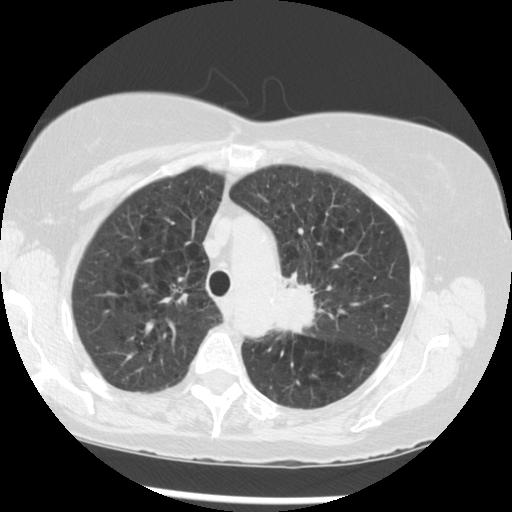
Axial slice from a low-dose chest CT screening exam, third annual screen, lung window (W 1500 / L -600 HU), 2.5 mm slice thickness, standard (soft-tissue) reconstruction kernel (STANDARD), 120 kVp. Female participant, aged 70 years at enrolment. Current smoker at enrolment.
Expert reader's lesion annotation, box from (x=266, y=266) to (x=360, y=356) px. Screening reader's record for this exam (one nodule recorded; not confirmed to be the boxed lesion): non-calcified nodule or mass ≥4 mm, left upper lobe, 32 × 26 mm, spiculated (stellate) margins, soft tissue attenuation, pre-existing on the prior screen: yes; interval growth: yes. Official screen result: positive, other. Later outcome: lung cancer diagnosed 24 days after this screen — neoplasm, malignant, left upper lobe, stage IIIB (AJCC 6th edition), 40 mm at pathology.